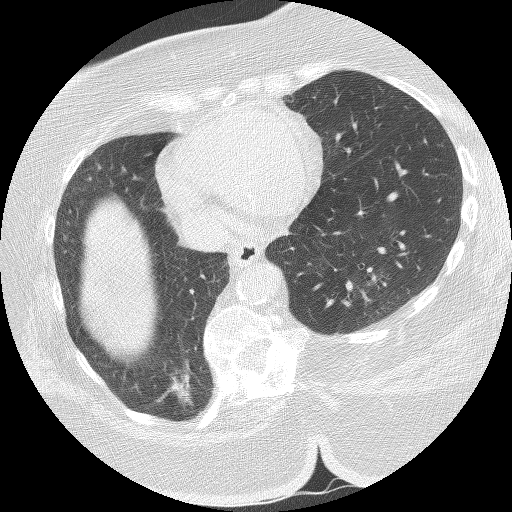
Axial slice from a low-dose chest CT screening exam; first (baseline) screen; lung window (W 1500 / L -600 HU); 2.5 mm slice thickness. Female, age 59 years at enrolment. Former smoker at enrolment.
Expert-annotated lung lesion, bounding box <145,346,203,415> (left, top, right, bottom; pixels). Screening reader's record for this exam (one nodule recorded; not confirmed to be the boxed lesion): non-calcified nodule or mass ≥4 mm, right lower lobe, 21 × 10 mm, spiculated (stellate) margins, soft tissue attenuation. Official screen result: positive, change unspecified: nodule(s) >= 4 mm or enlarging nodule(s), mass(es), or other non-specific abnormalities suspicious for lung cancer.